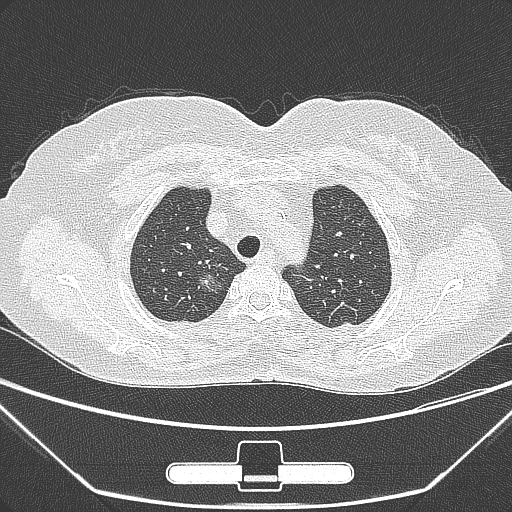
Chest CT, one axial slice. Position 228 of 275 along the scan axis. 120 kVp. Lung window (W 1500 / L -600 HU). 512 × 512 image matrix, field of view 356 × 356 mm. Patient: female, 63 years. From the clinical record (not read from this slice): clinical TNM (as recorded): T1a N0 M0; histopathological grade: G1.
Annotated regions visible in this slice (rectangle marked by the reading radiologist):
- lung tumour (recorded histology: adenocarcinoma): box from (x=187, y=261) to (x=227, y=306) px